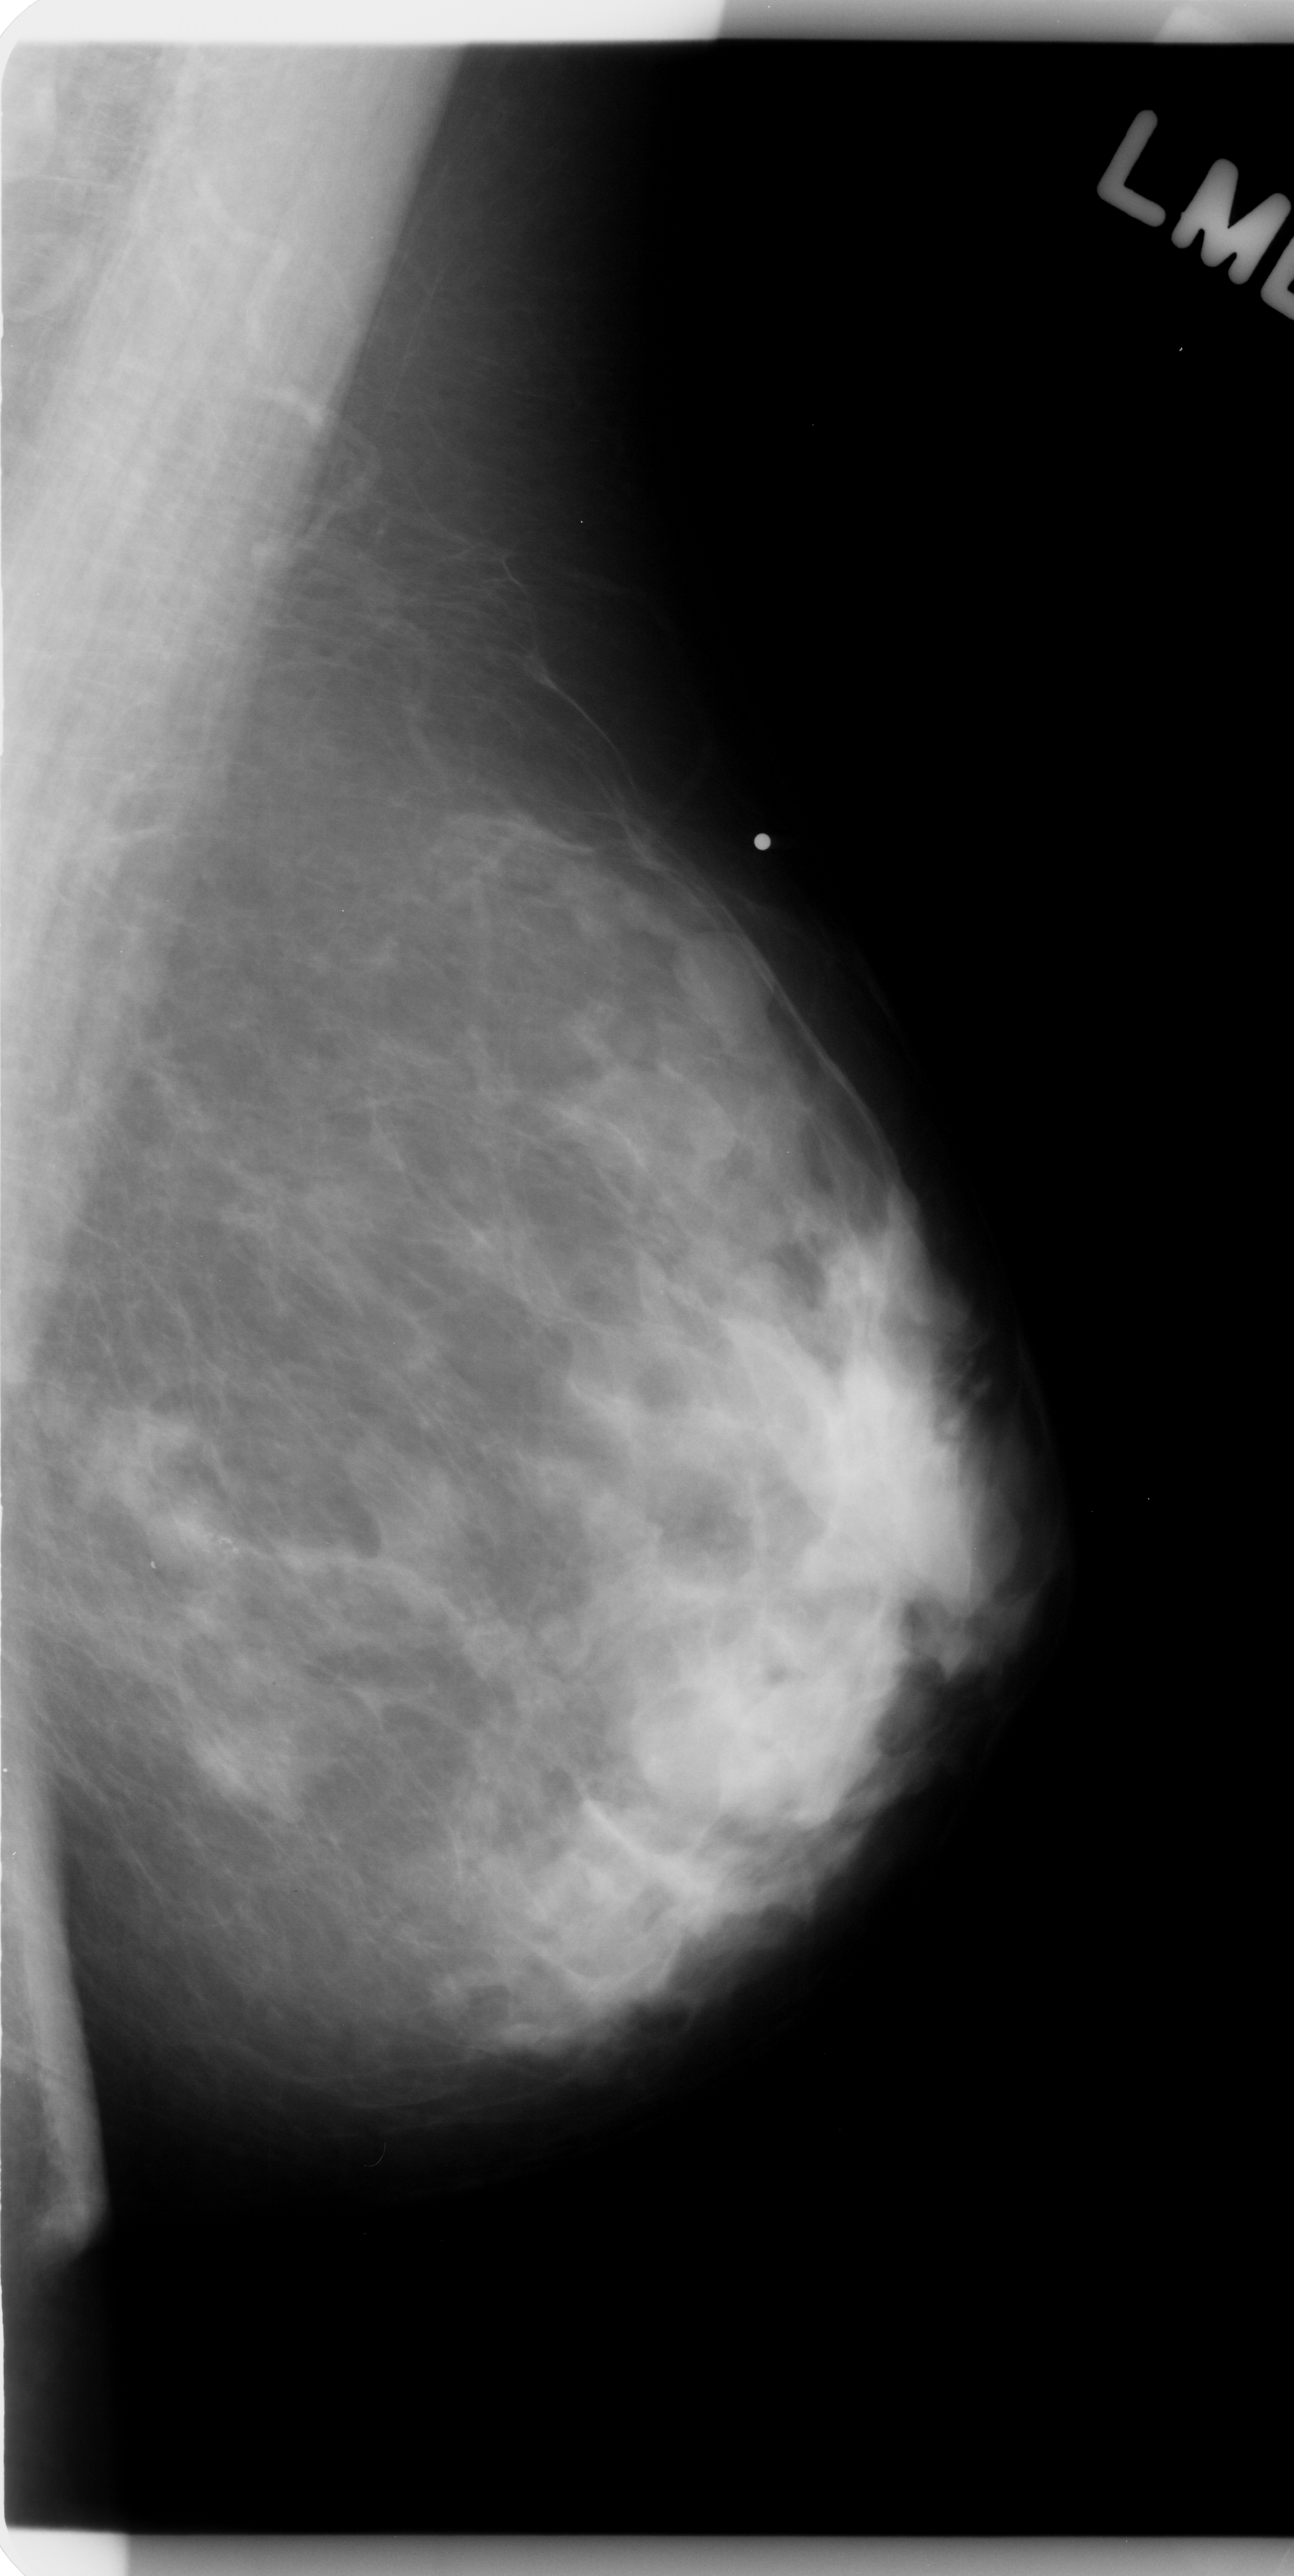
Digitized screen-film mammogram; left breast; mediolateral oblique (MLO) view; BI-RADS breast density category 3 (scale 1–4).
Finding: mass, shape oval, margins circumscribed; BI-RADS assessment category 3; subtlety rating 5 on a 1 (subtle) to 5 (obvious) scale; pathology (as recorded): benign.